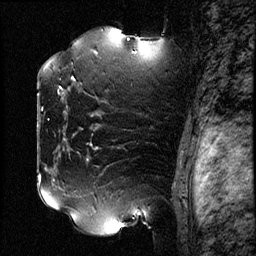
Breast MRI (dynamic contrast-enhanced), one sagittal slice; slice 59 of 78 in the series (ordered by position); dynamic contrast-enhanced study with each time point stored as its own series, time point 2 of 3 at this slice position (early post-contrast, ordered by acquisition time); 1.5 T; TE 4.2 ms, TR 17.6 ms; 2 mm slice thickness; 256 × 256 image matrix, field of view 200 × 200 mm. Patient: female, 42 years. From the clinical record (not read from this slice): setting: breast cancer imaged before/during neoadjuvant chemotherapy; receptor status: HER2-positive.
Annotated regions visible in this slice (semi-automatic segmentation, software-assisted and operator-edited):
- analysis volume of interest (the breast-tissue region the enhancement analysis was run in; not a lesion): bounding box [x1, y1, x2, y2] px = [50, 48, 131, 129]
- tumour enhancement mask (voxels above the 100 % enhancement threshold inside the analysis volume of interest): [60, 77, 75, 89]